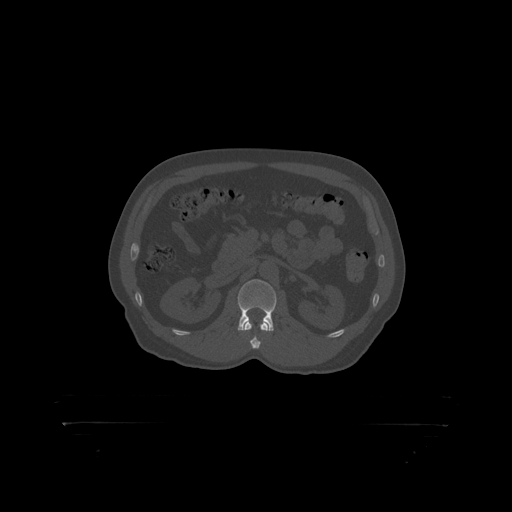
CT including the spine, one axial slice. Slice 307 of 399 in the series (ordered by position). 120 kVp. Bone window (W 1800 / L 400 HU). 1.25 mm slice thickness. 512 × 512 image matrix, field of view 650 × 650 mm. Male patient, age 46 years. Case-level facts recorded for this patient, not image findings: primary cancer: skin.
Annotated regions visible in this slice (semi-automatically segmented with operator editing):
- L2 vertebra: bounding box (x1, y1, x2, y2) in pixels: (238, 280, 277, 319)